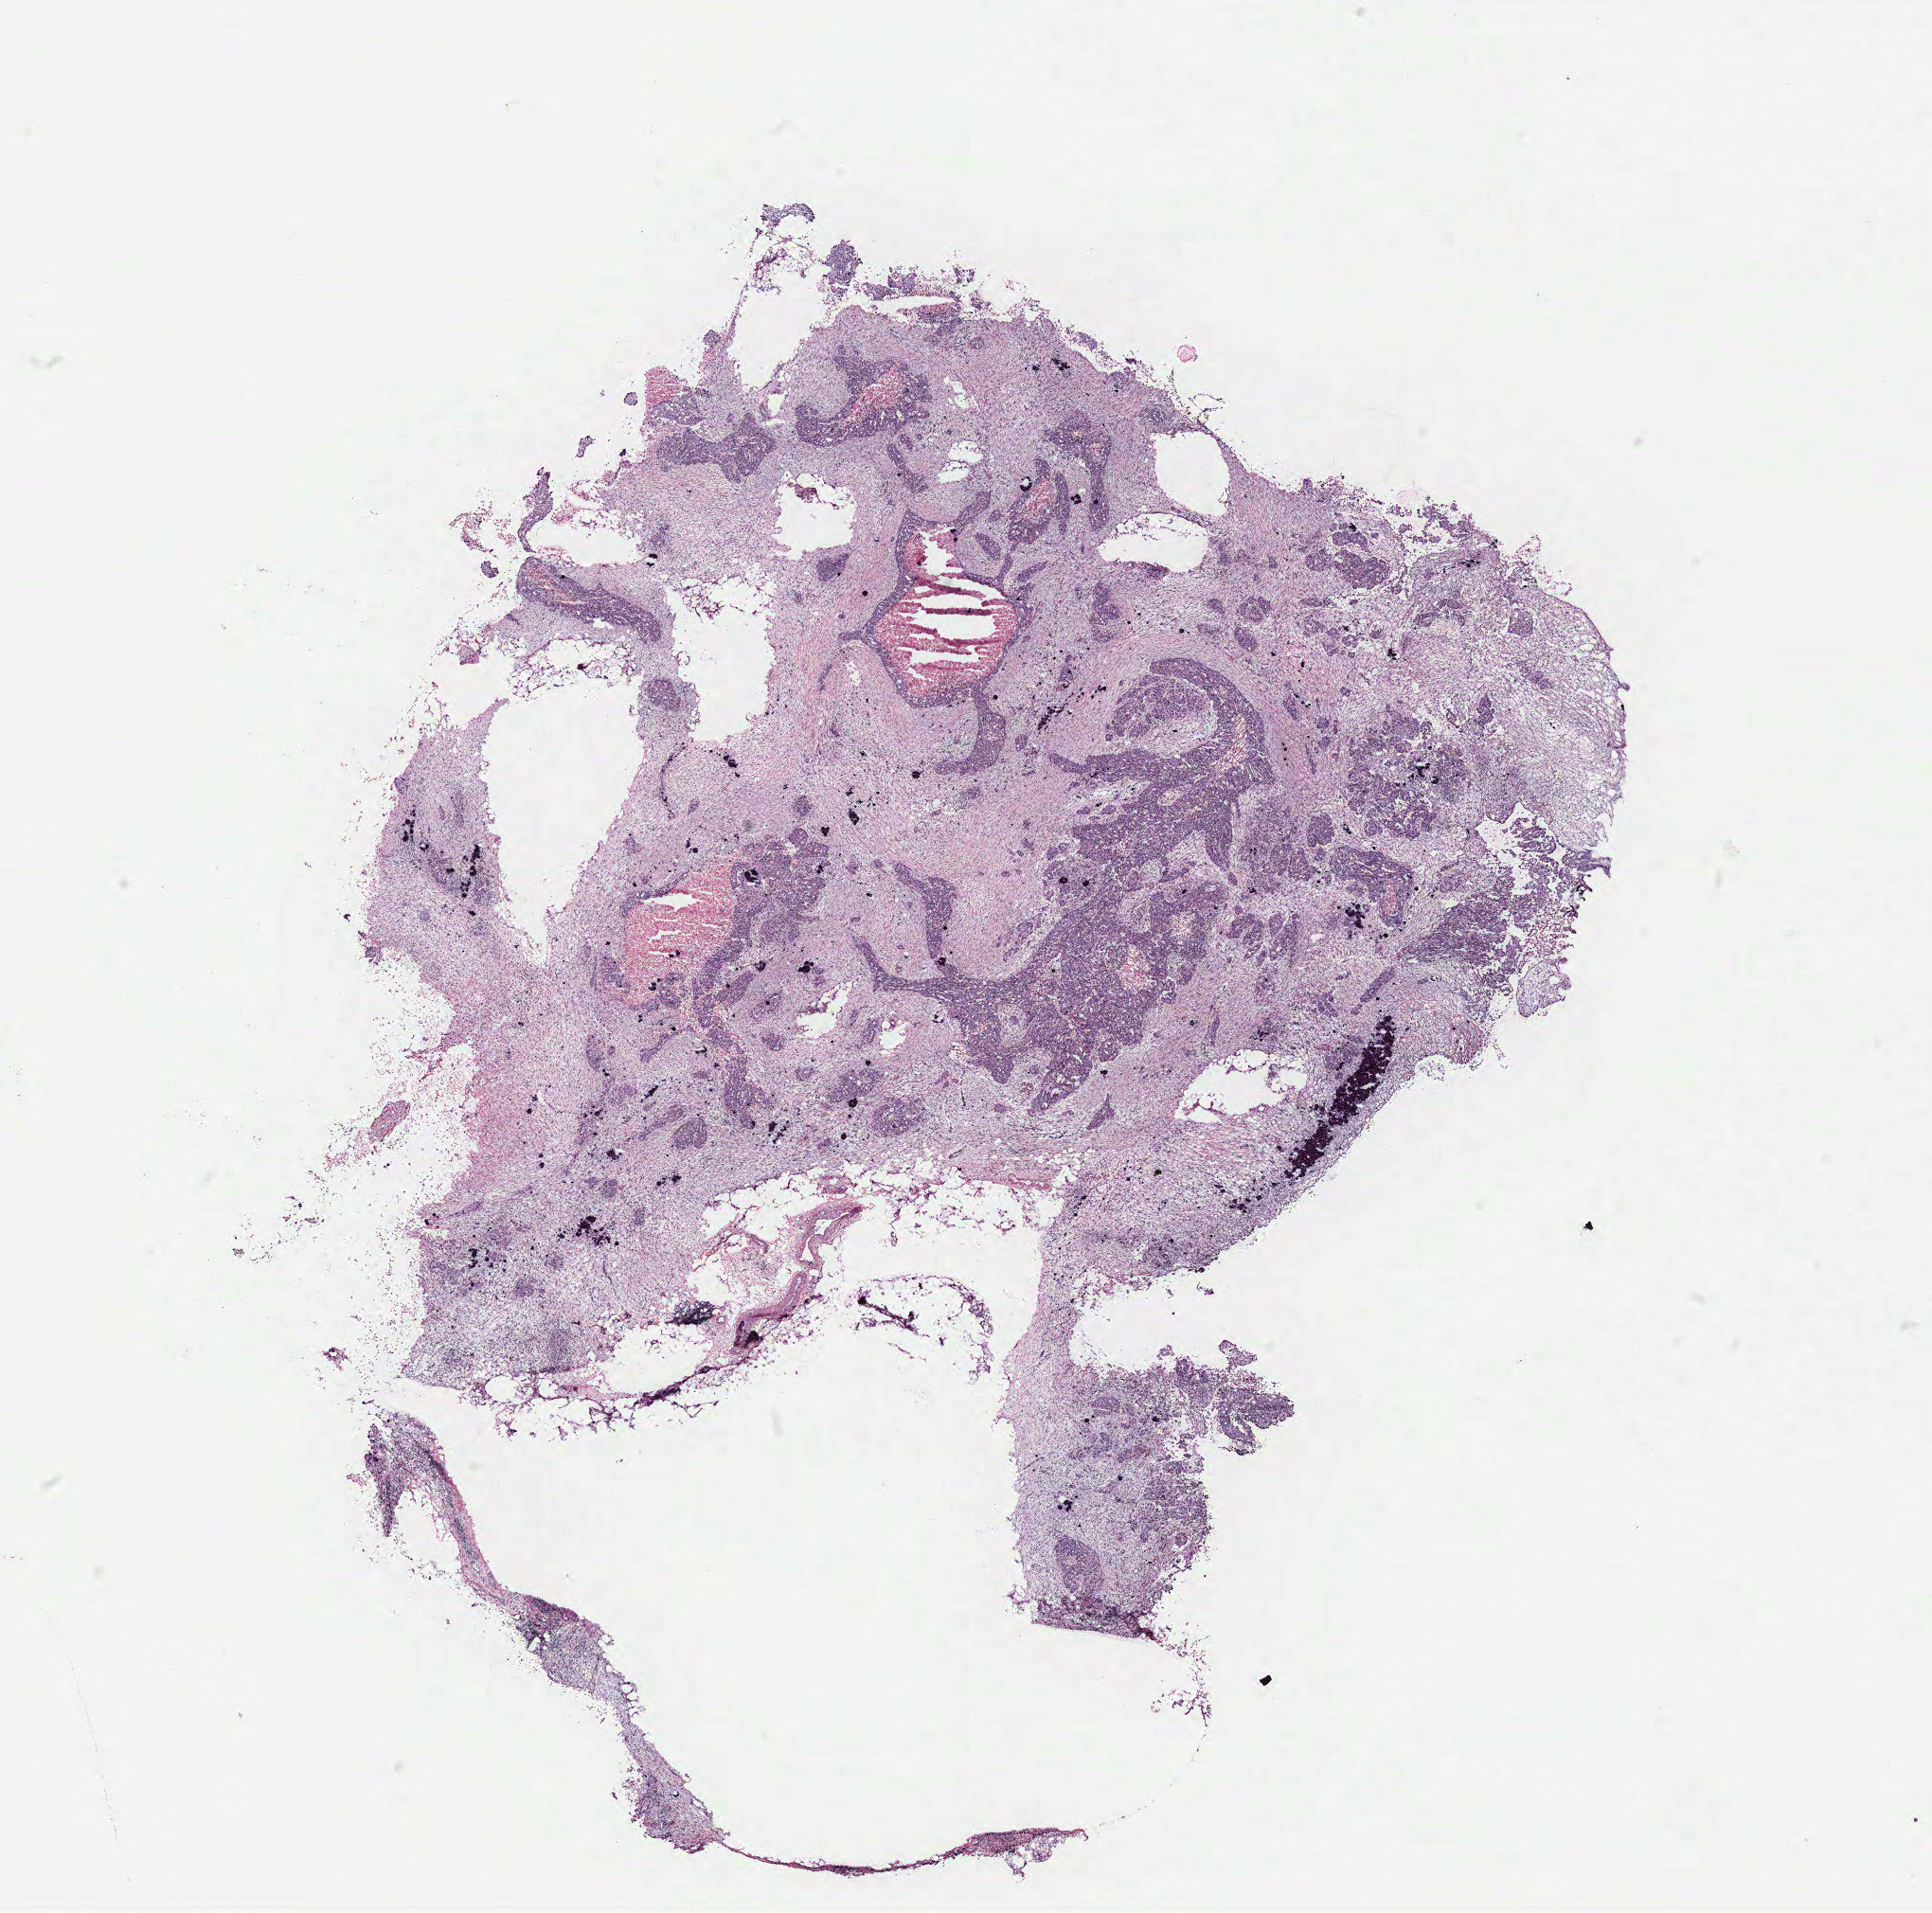
H&E whole-slide image, shown as a low-resolution overview of the whole scanned area (about 16.3 x 16.2 mm). Tumour tissue sample, ovary. 53-year-old female patient.
* histologic diagnosis: Serous adenocarcinoma, NOS (fallopian tube)
* primary tumour site (as recorded): fallopian tube